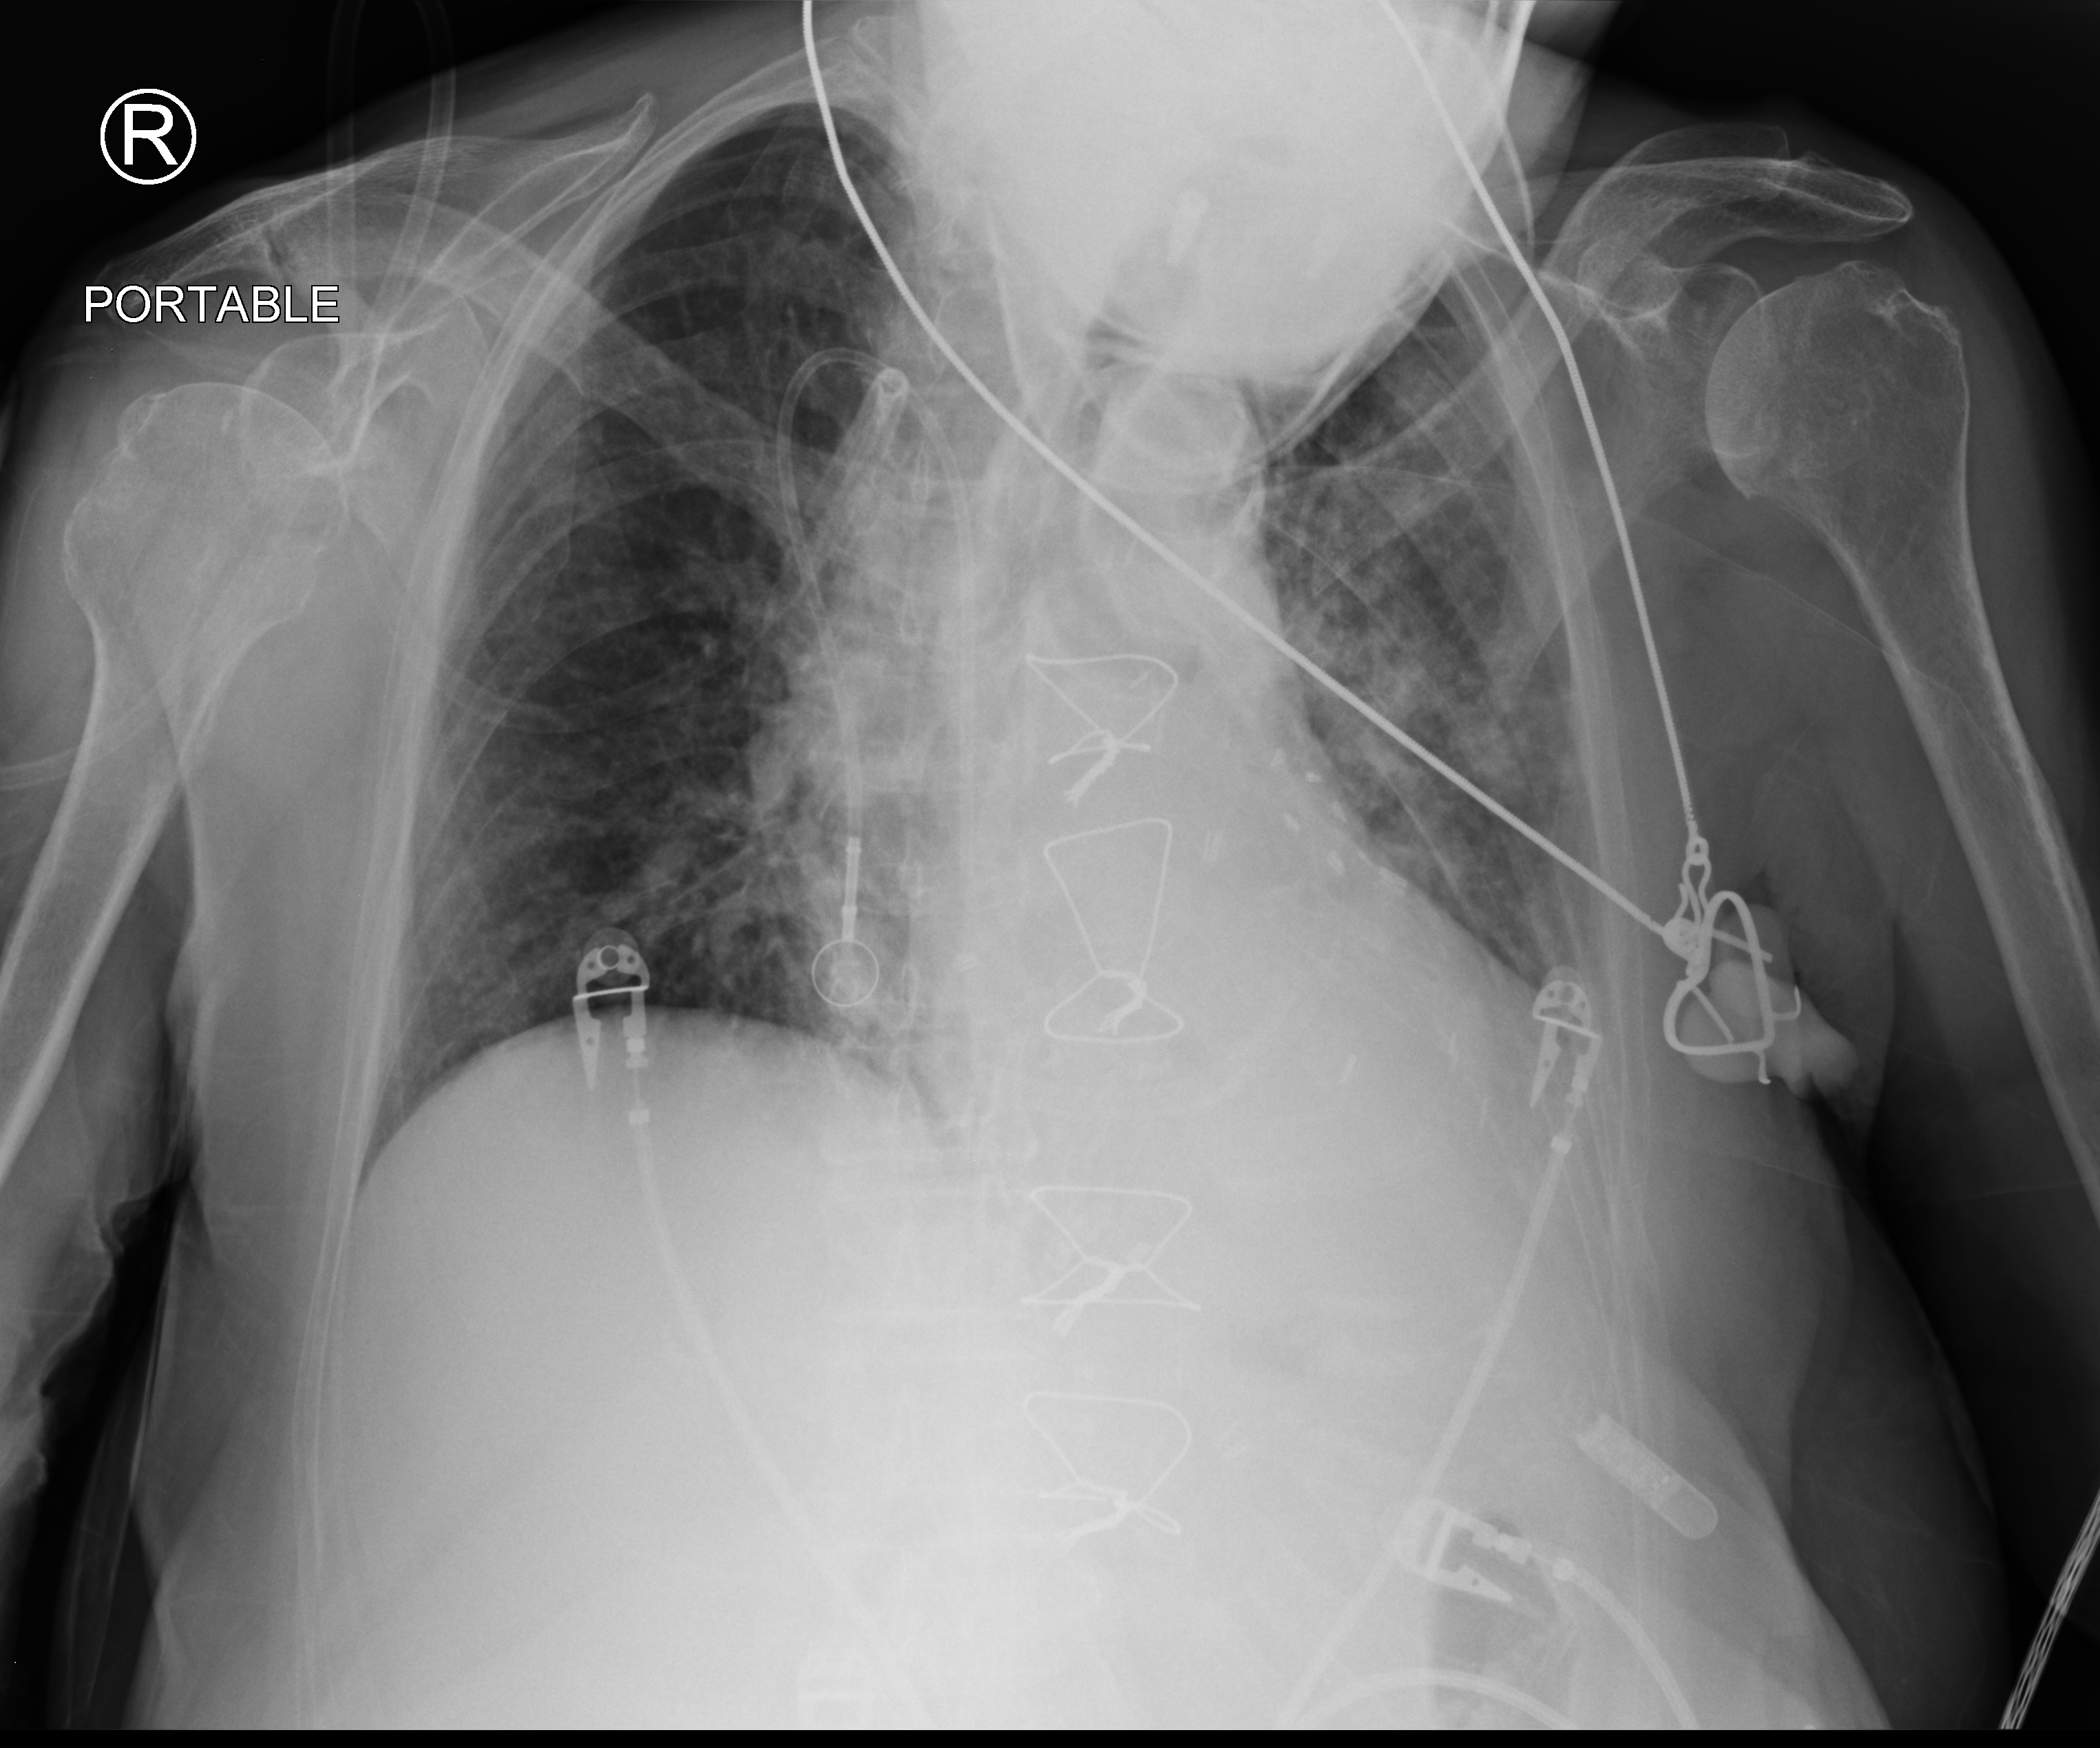
Bedside chest radiograph (computed radiography), anteroposterior (AP) projection. Patient hospitalised with COVID-19; female, aged 75–90 years.
Admission-level facts for this patient (not findings on this image; timing relative to this image not recorded):
- admitted to intensive care during this hospital stay: no
- other chronic lung disease (admission record): no
- mechanically ventilated during this hospital stay: no